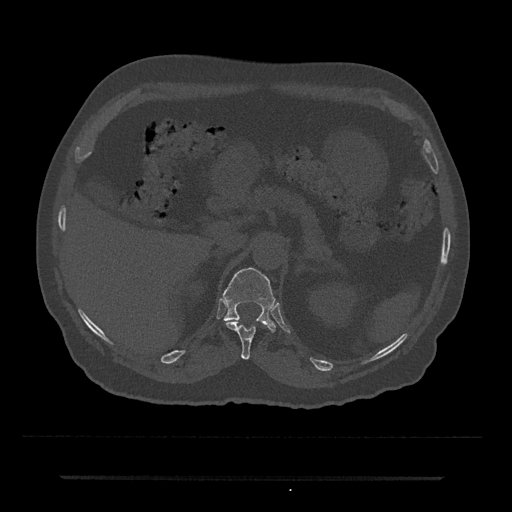
CT including the spine, one axial slice. Slice 149 of 797 in the series (ordered by position). Reconstruction kernel Br40s/3. Bone window (W 1800 / L 400 HU). 0.5 mm slice thickness. 512 × 512 image matrix, field of view 437 × 437 mm. Patient: male, 69 years. From the clinical record (not read from this slice): primary cancer: prostate.
Annotated regions visible in this slice (semi-automatic segmentation, software-assisted and operator-edited):
- T11 vertebra: bounding box <225,321,256,360> (left, top, right, bottom; pixels)
- T12 vertebra: <223,267,276,332>